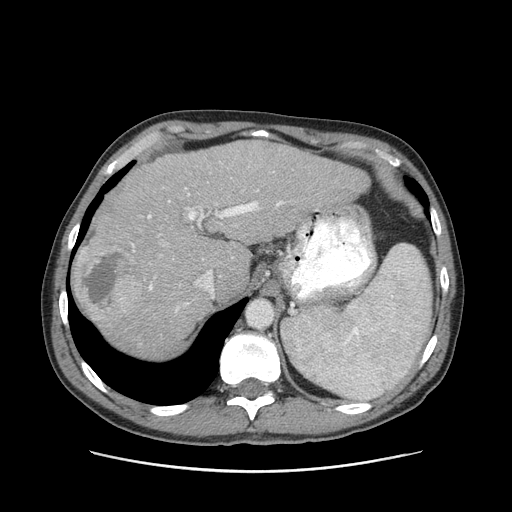
Contrast-enhanced abdominal CT (liver protocol), one axial slice. Position 72 of 93 along the scan axis. Reconstruction kernel STANDARD. Soft-tissue window (W 400 / L 40 HU). 2.5 mm slice thickness. 512 × 512 image matrix, field of view 380 × 380 mm. From the clinical record (not read from this slice): diagnosis: hepatocellular carcinoma (patient treated with transarterial chemoembolisation; whether this scan precedes or follows treatment is not stated here); TNM stage (as recorded): Stage-II; Child-Pugh class: A; tumour nodularity: multinodular.
Annotated regions visible in this slice (semi-automatically segmented with operator editing):
- abdominal aorta: bounding box [x1, y1, x2, y2] px = [247, 300, 271, 326]
- liver parenchyma outside the tumour (the mass and vessels are separate outlines, so this box may not span the whole liver): [72, 140, 368, 356]
- mass: [73, 236, 143, 324]
- liver vessels: [132, 188, 284, 312]